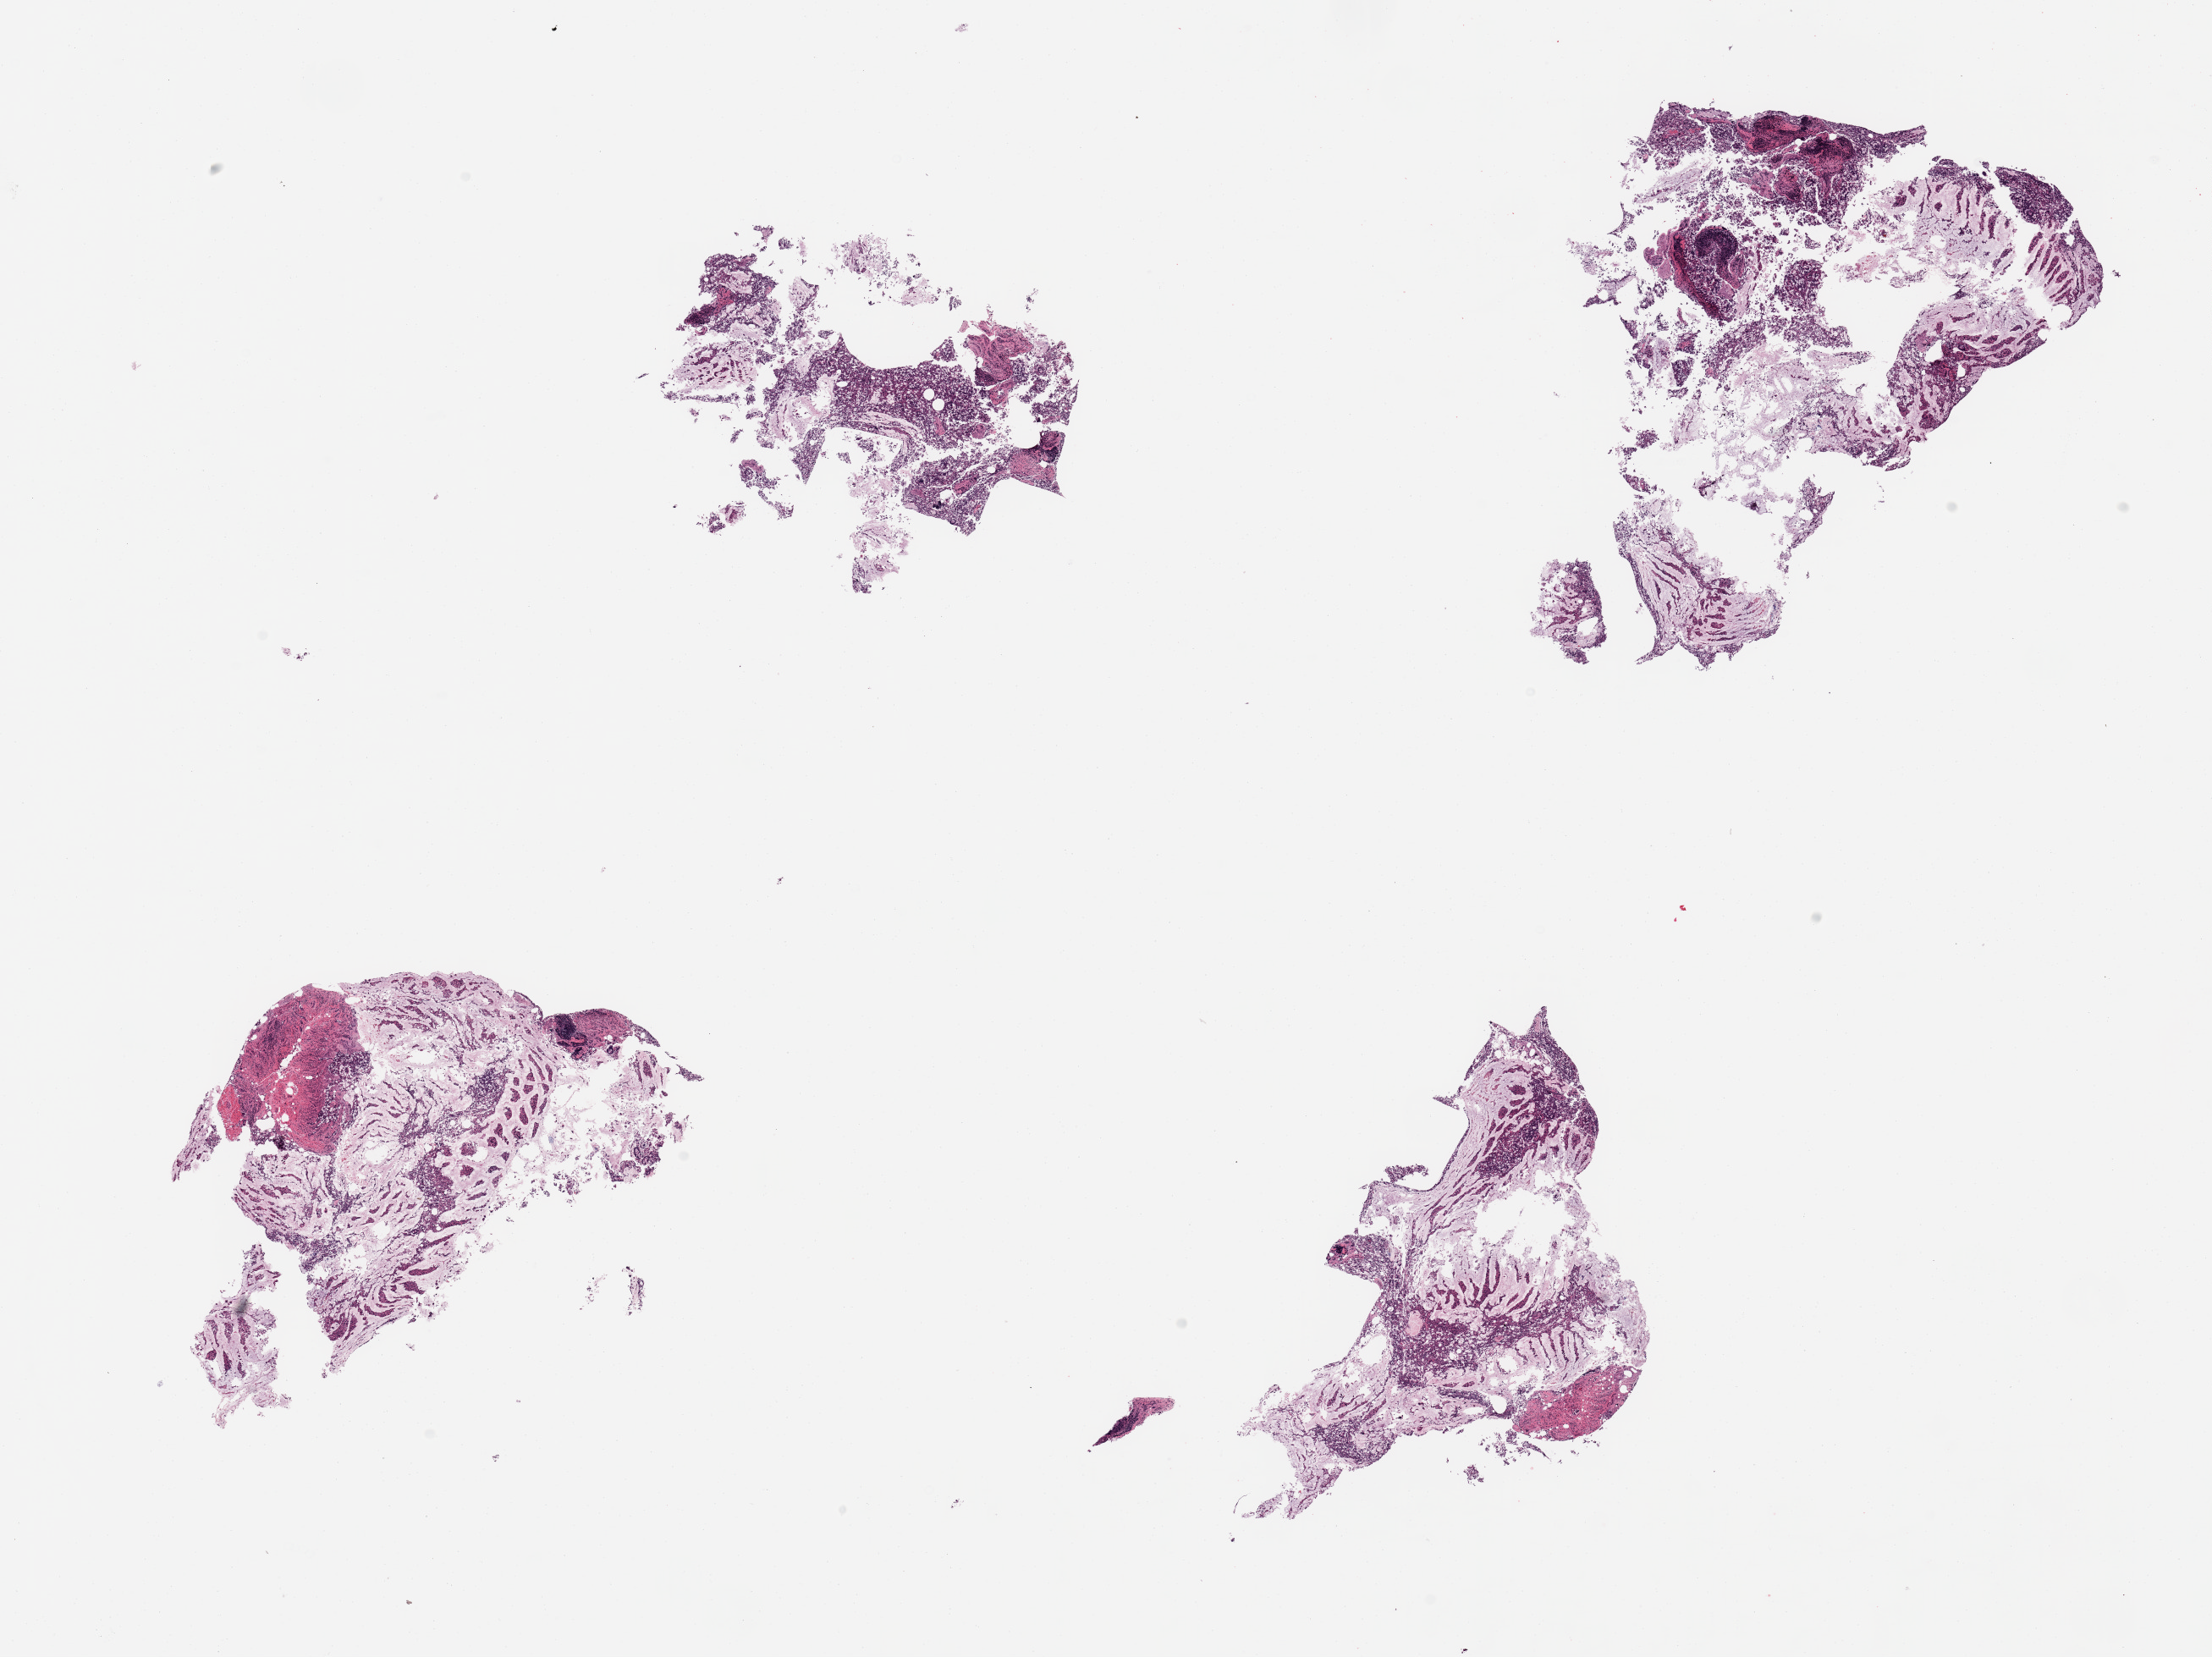
H&E whole-slide image, shown as a low-resolution overview of the whole scanned area (about 20.7 x 15.5 mm). Donor sex: female.
- specimen: PAXgene-fixed, paraffin-embedded tissue; section of ileum (target tissue); donor tissue sample